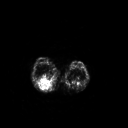
FDG PET of an extremity soft-tissue mass (from a PET/CT study), one axial slice. Position 169 of 267 along the scan axis. 128 × 128 image matrix, field of view 500 × 500 mm. Patient: female, 62 years. Case-level facts recorded for this patient, not image findings: histological type: liposarcoma; site of the primary tumour: right thigh.
Outlined on this slice (expert contour drawn on MRI and transferred to this co-registered scan by the dataset authors):
- gross tumour volume (mass): box from (x=38, y=76) to (x=53, y=91) px